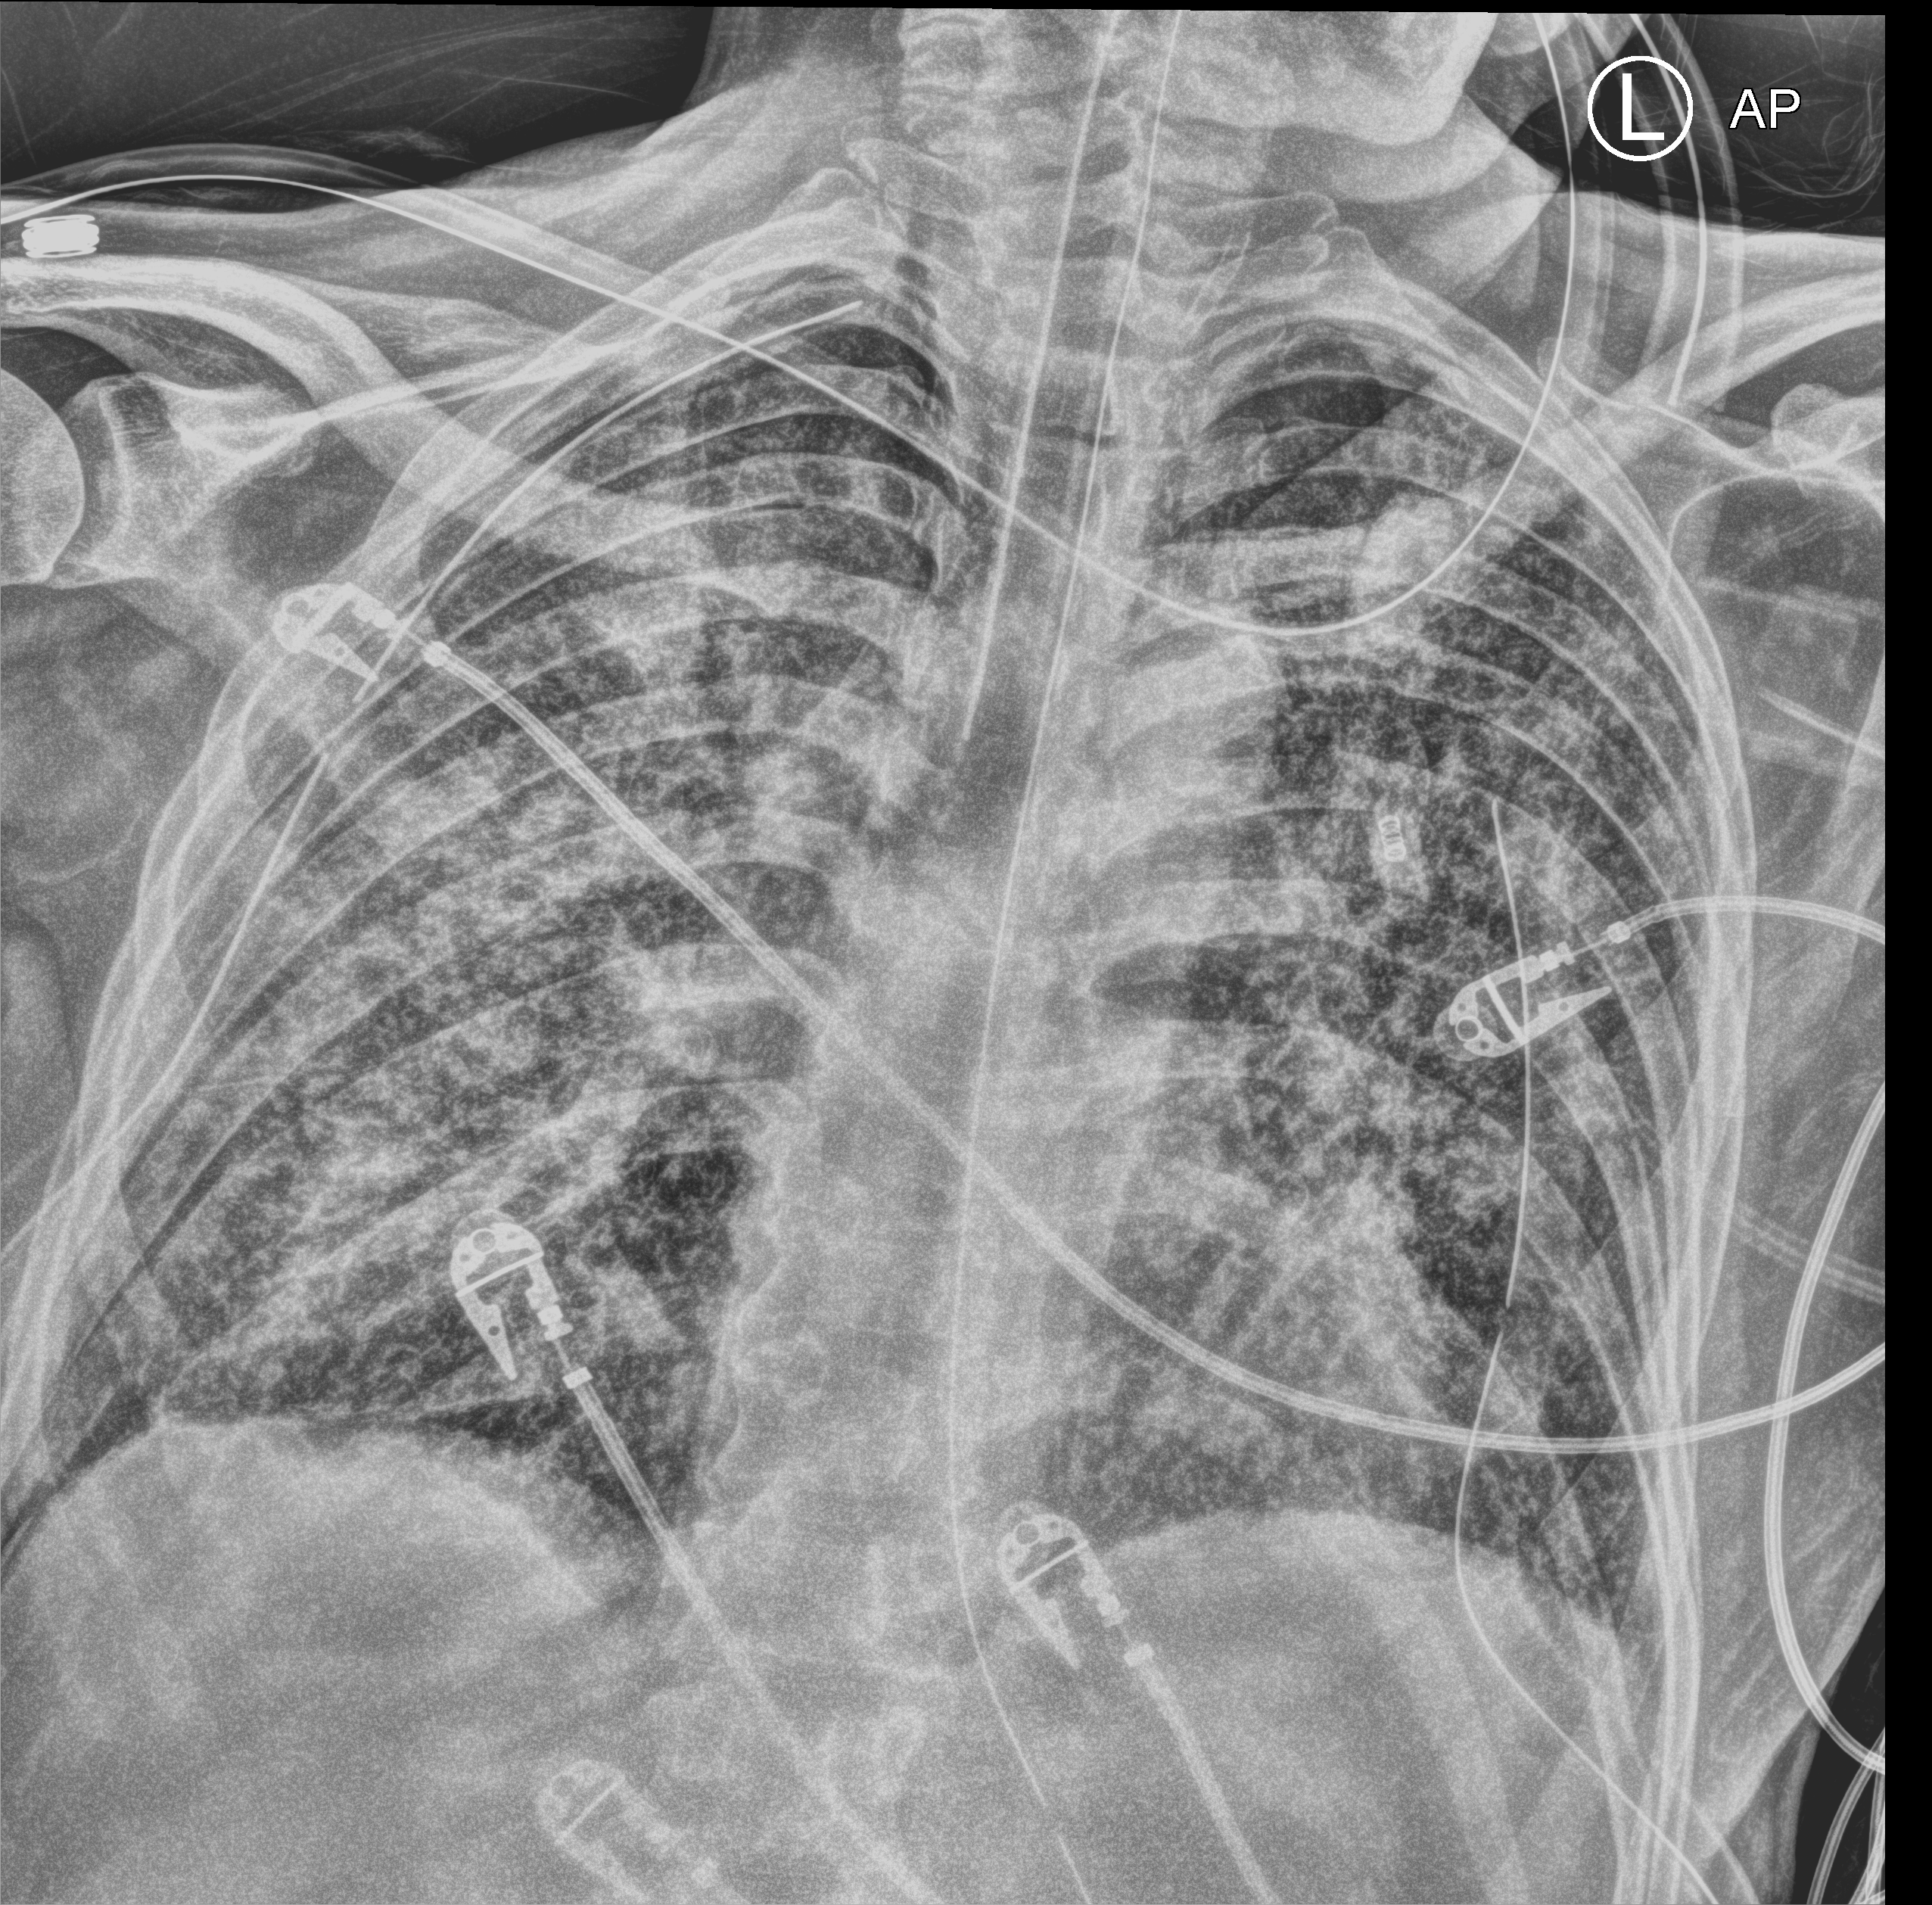
Portable chest radiograph; anteroposterior (AP) projection. Patient hospitalised with COVID-19; male, aged 60–74 years.
From the hospital-stay record, not from the radiograph (when in the stay this image was taken is not recorded): mechanically ventilated during this hospital stay: yes; smoking status (admission record): never.